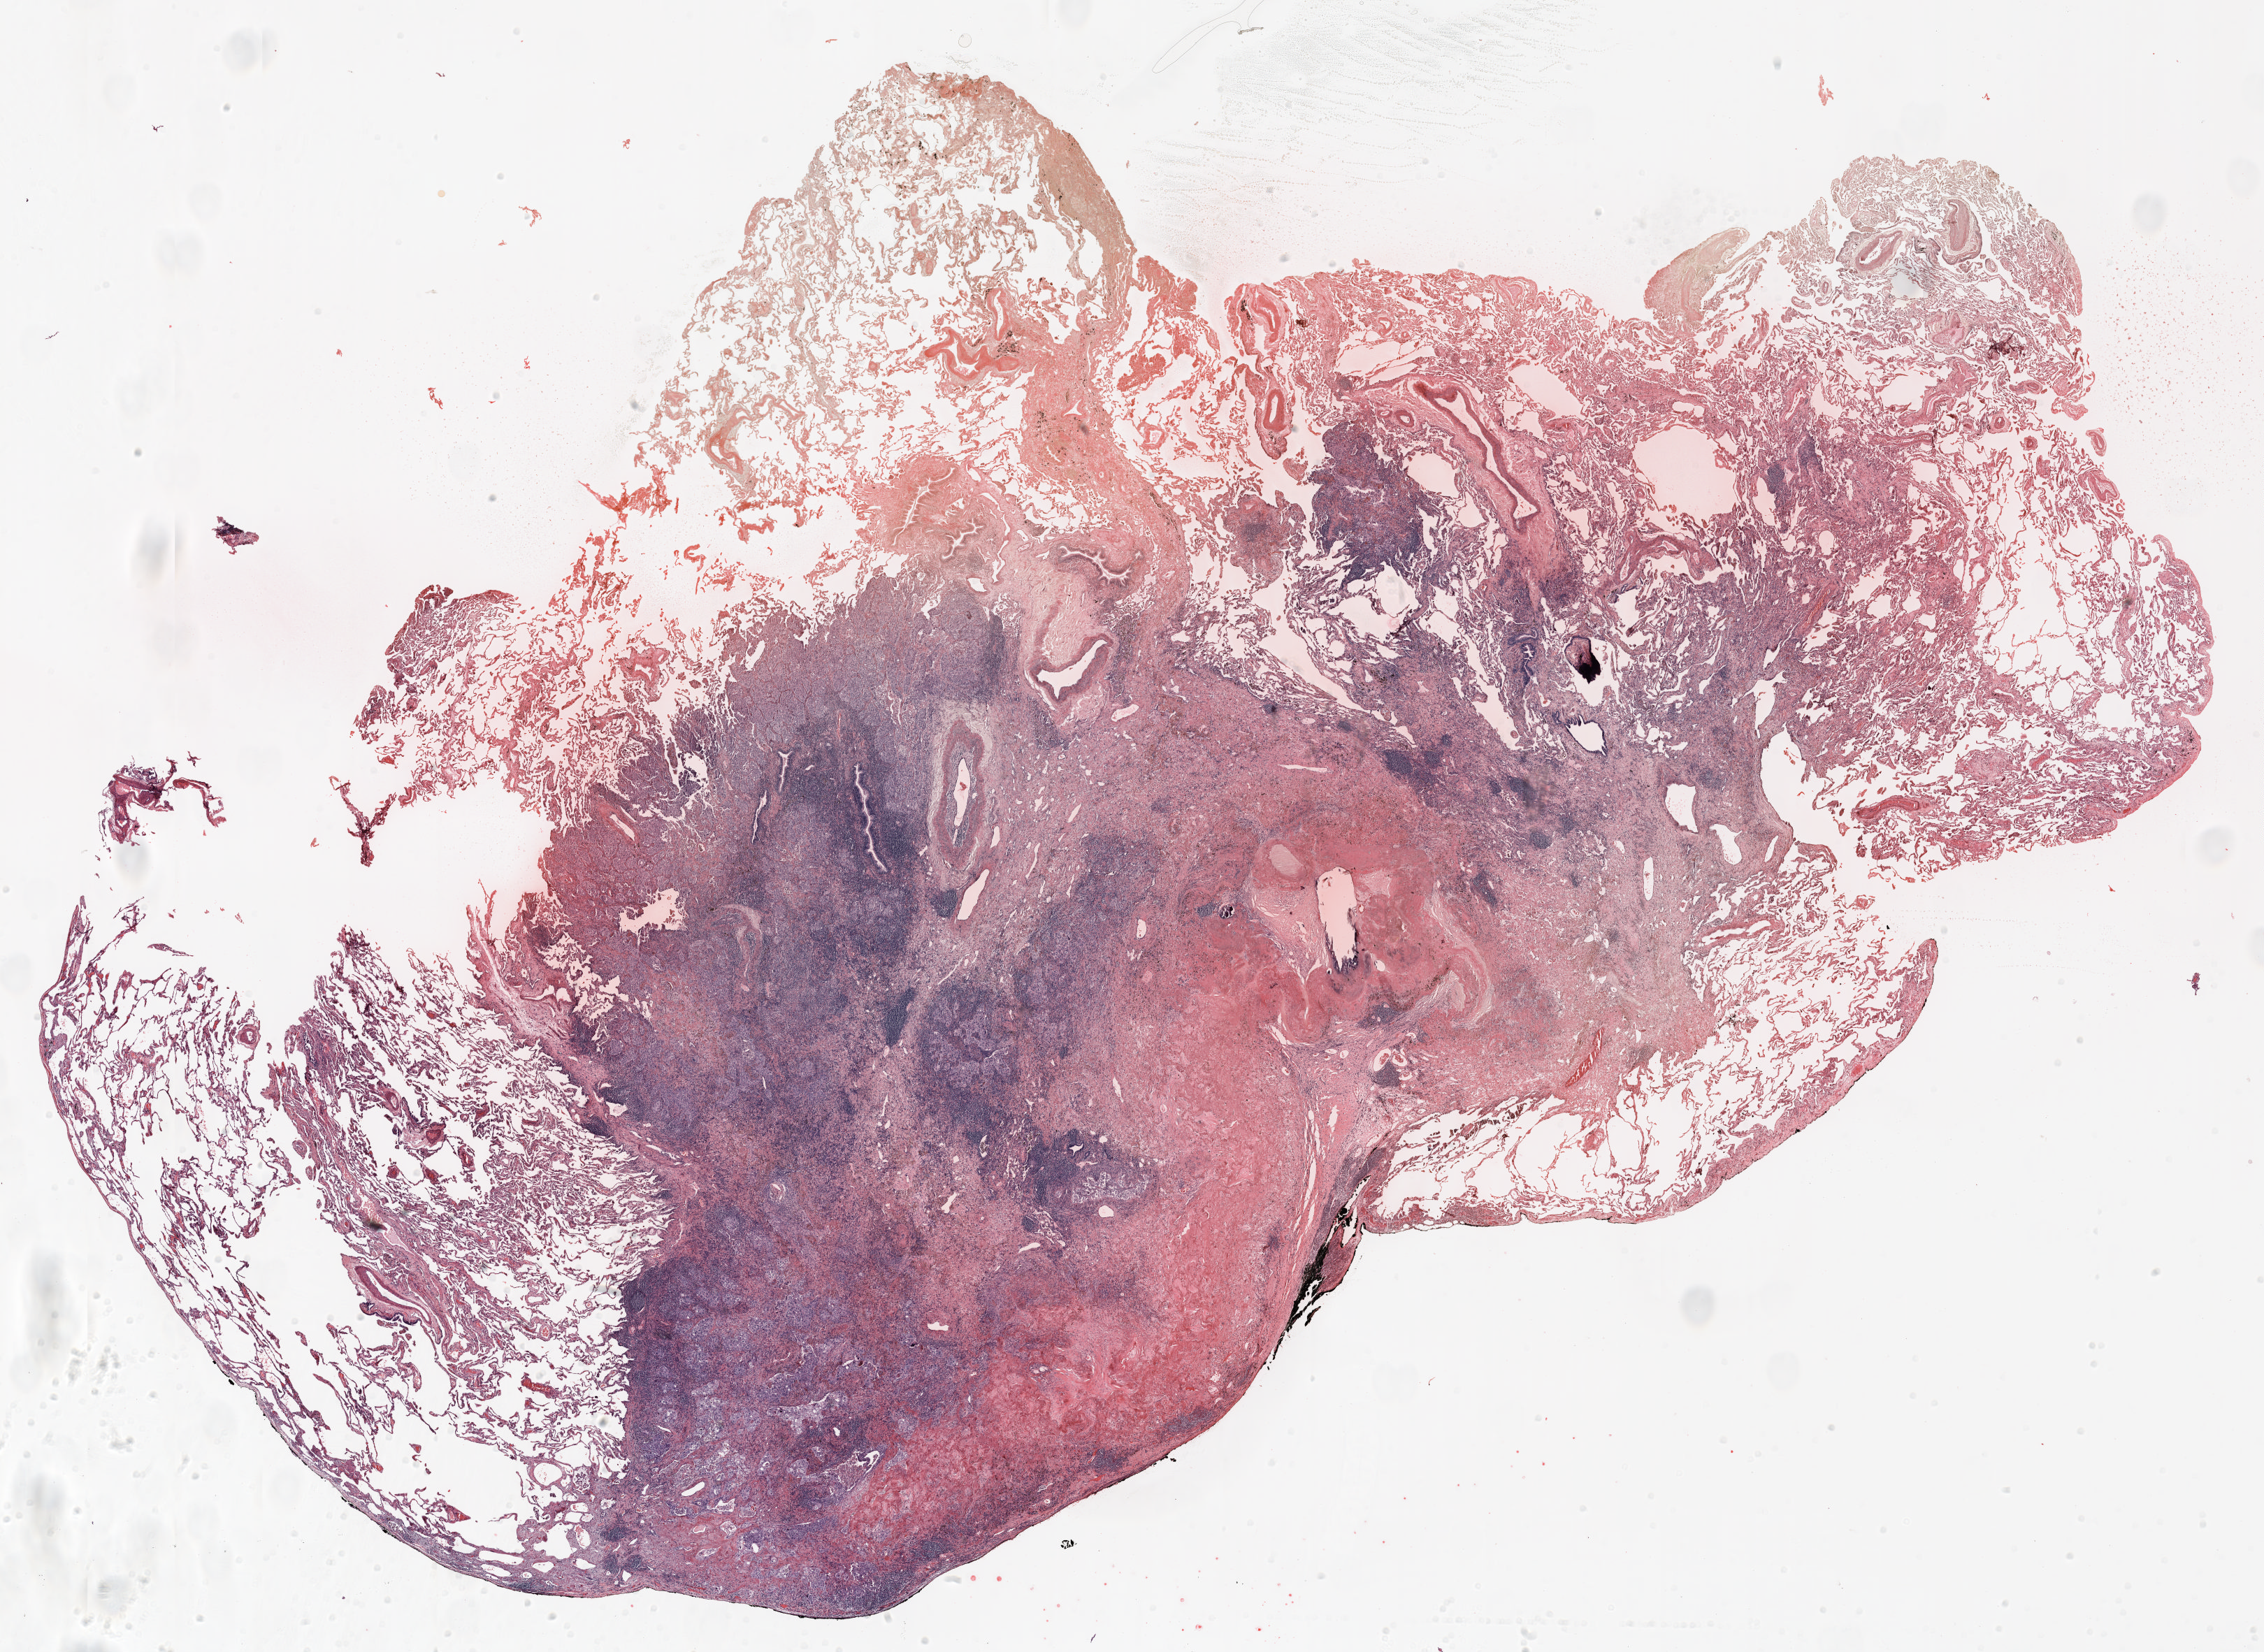
H&E-stained whole-slide image, a low-resolution overview of the entire scanned area, about 26.0 x 19.0 mm (slide scanned at 20x). FFPE section. Lung. Male, age 61 at enrolment. Current smoker at enrolment. Grade: poorly differentiated (G3).
Stage (AJCC 6th edition): IIIA. Tumour size (pathology): 30 mm. Primary tumour location (clinical record): left upper lobe. ICD-O-3 topography: upper lobe of lung (C34.1). Participant's lung-cancer diagnosis: Adenocarcinoma, NOS.